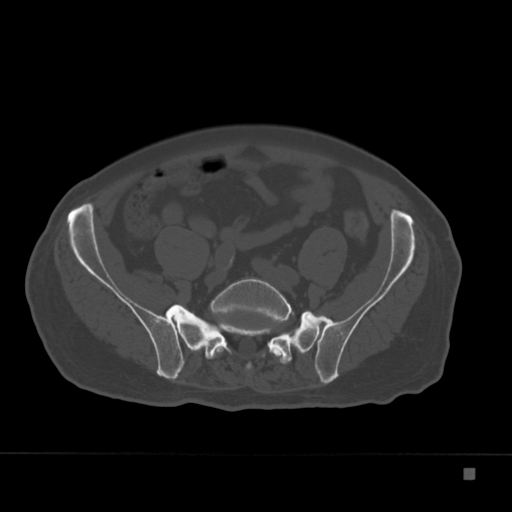
CT including the spine, one axial slice; position 13 of 332 along the scan axis; reconstruction kernel Br40s; 120 kVp; bone window (W 1800 / L 400 HU); 512 × 512 image matrix, field of view 389 × 389 mm. Male patient, age 72 years. From the clinical record (not read from this slice): primary cancer: skeletal.
Structures marked on this image (semi-automatically segmented with operator editing):
- L5 vertebra: bounding box (x1, y1, x2, y2) in pixels: (208, 278, 291, 369)